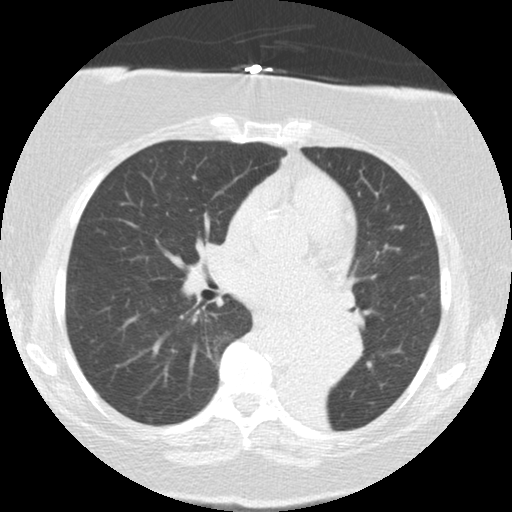
Low-dose screening chest CT, axial slice, baseline screening round, lung window (W 1500 / L -600 HU), 2.5 mm slice thickness, standard (soft-tissue) reconstruction kernel (STANDARD). Female participant, aged 71 years at enrolment.
- Expert-annotated lung lesion, bounding box [x1, y1, x2, y2] px = [285, 306, 364, 383].
- Reader record for this screening exam (exam-level; its link to the box is not recorded): non-calcified nodule or mass ≥4 mm, right middle lobe, 5 × 5 mm, smooth margins, soft tissue attenuation.
- Note: the box lies in the patient's left hemithorax on this image, whereas the reader's record names the right lung; they may be different findings.
- Official screen result: positive, change unspecified: nodule(s) >= 4 mm or enlarging nodule(s), mass(es), or other non-specific abnormalities suspicious for lung cancer.
- Later outcome: lung cancer diagnosed 46 days after this screen — large cell carcinoma, NOS, left lower lobe, mediastinum, other location, poorly differentiated (G3), stage IV (AJCC 6th edition), 50 mm at pathology.